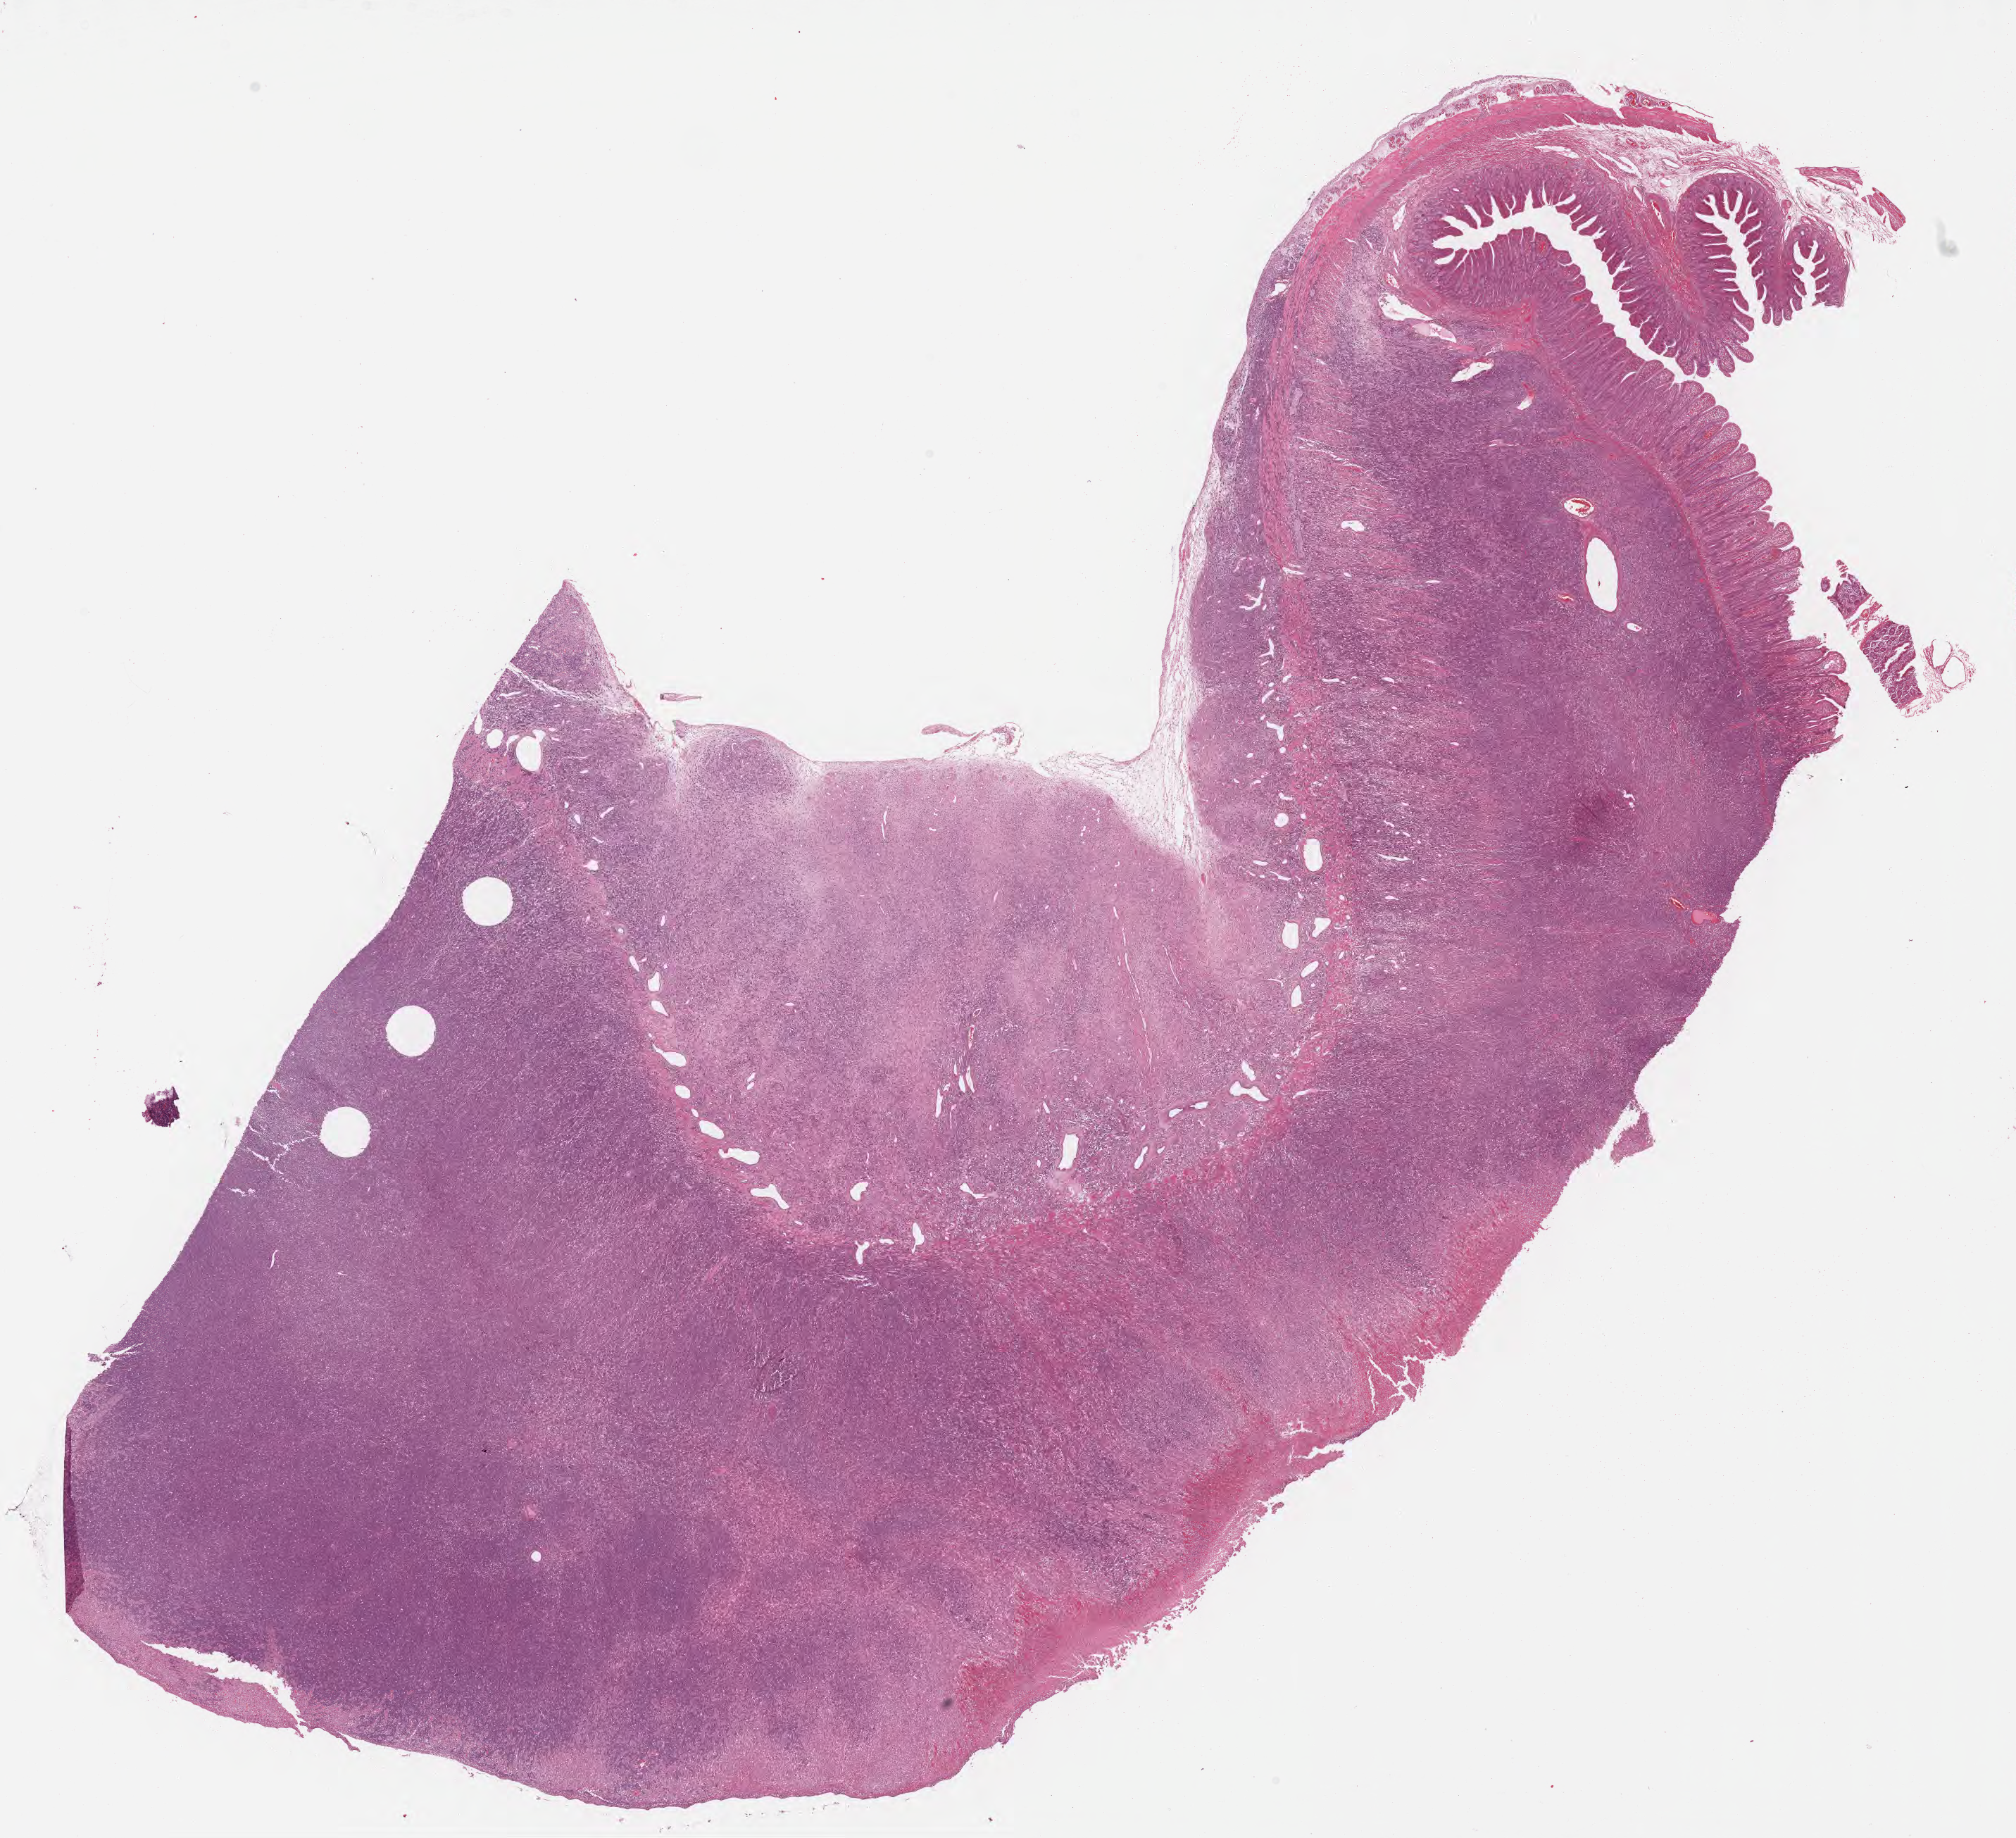
Whole-slide image, H&E stain, shown as a low-resolution overview of the whole scanned area (about 23.1 x 21.1 mm); formalin-fixed, paraffin-embedded (FFPE) tissue; specimen: primary tumor. Male patient; age at initial diagnosis 4 years.
Histologic diagnosis: Burkitt lymphoma, NOS.